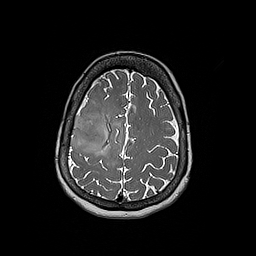
Brain MRI from a brain-tumour surgery series, one axial slice; slice 59 of 192 in the series (ordered by position); 1 mm slice thickness; 256 × 256 image matrix, field of view 250 × 250 mm. From the clinical record (not read from this slice): histopathology: Oligodendroglioma; WHO grade: 3; IDH mutation: yes.
Outlined on this slice (manually delineated by an expert):
- tumour: bounding box <71,115,107,153> (left, top, right, bottom; pixels)